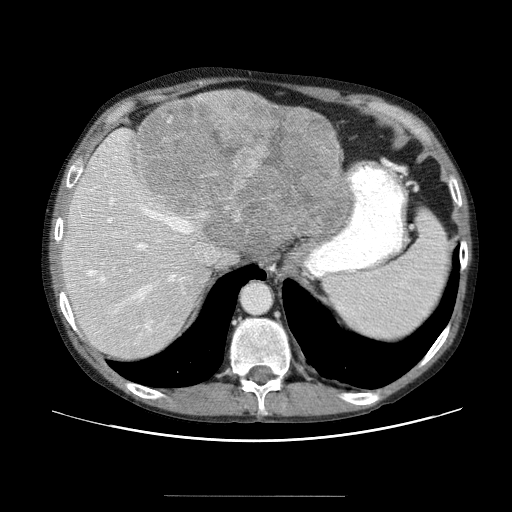
Contrast-enhanced abdominal CT (liver protocol), one axial slice. Slice 44 of 69 in the series (ordered by position). Reconstruction kernel STANDARD. 120 kVp. Soft-tissue window (W 400 / L 40 HU). 2.5 mm slice thickness. 512 × 512 image matrix. From the clinical record (not read from this slice): diagnosis: hepatocellular carcinoma (patient treated with transarterial chemoembolisation; whether this scan precedes or follows treatment is not stated here); TNM stage (as recorded): Stage-IVB; Child-Pugh class: B; tumour differentiation: poorly differentiated.
Outlined on this slice (semi-automatically segmented with operator editing):
- liver parenchyma outside the tumour (the mass and vessels are separate outlines, so this box may not span the whole liver): bounding box (x1, y1, x2, y2) in pixels: (60, 100, 342, 362)
- mass: (133, 89, 350, 269)
- liver vessels: (77, 202, 185, 327)